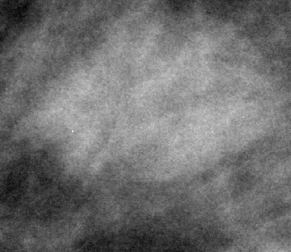
Cropped region of a digitized screen-film mammogram centred on a radiologist-marked abnormality, right breast, CC view.
- Finding: mass, shape oval, margins circumscribed; BI-RADS assessment category 3; subtlety rating 4 on a 1 (subtle) to 5 (obvious) scale; pathology (as recorded): benign.